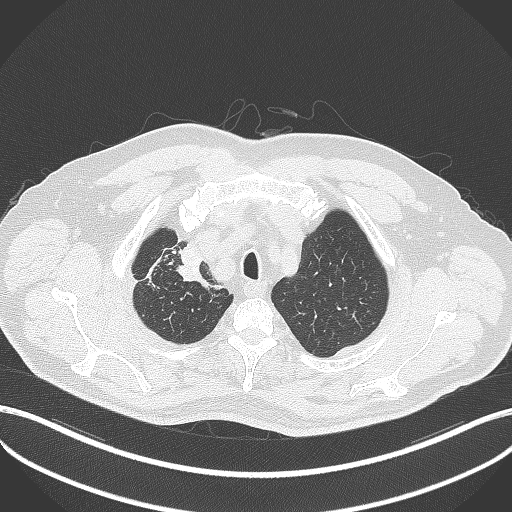
Chest CT, one axial slice. Slice 332 of 411 in the series (ordered by position). Reconstruction kernel B70f. 120 kVp. Lung window (W 1500 / L -600 HU). 1 mm slice thickness. 512 × 512 image matrix, field of view 400 × 400 mm. Patient: male, 60 years. Case-level facts recorded for this patient, not image findings: clinical TNM (as recorded): T1b N1 M0.
Annotated regions visible in this slice (bounding box drawn by a radiologist):
- lung tumour (recorded histology: squamous cell carcinoma): bounding box (x1, y1, x2, y2) in pixels: (178, 242, 227, 294)